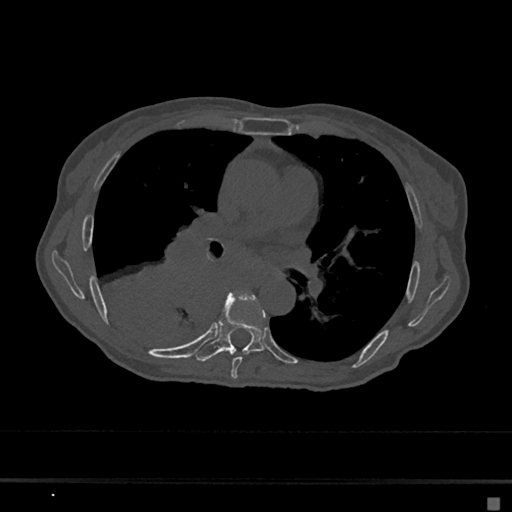
CT including the spine, one axial slice. Position 391 of 797 along the scan axis. Bone window (W 1800 / L 400 HU). 0.5 mm slice thickness. 512 × 512 image matrix, field of view 360 × 360 mm. Female patient, age 68 years. From the clinical record (not read from this slice): primary cancer: renal.
Structures marked on this image (semi-automatic segmentation, software-assisted and operator-edited):
- T6 vertebra: bounding box [x1, y1, x2, y2] px = [231, 292, 265, 379]
- T7 vertebra: [196, 293, 264, 362]